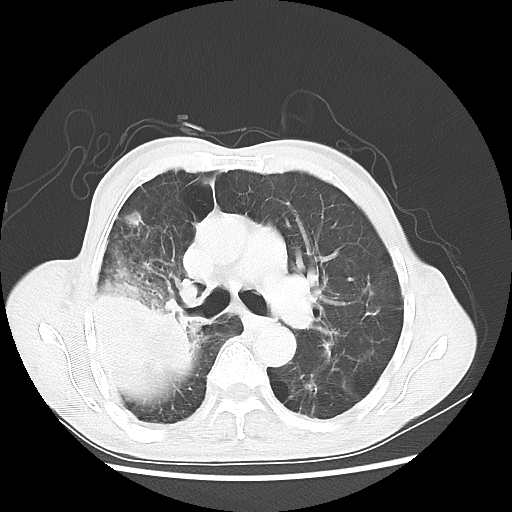
Chest CT, one axial slice; slice 33 of 58 in the series (ordered by position); 100 kVp; lung window (W 1500 / L -600 HU); 512 × 512 image matrix, field of view 351 × 351 mm. Male patient, age 75 years. From the clinical record (not read from this slice): clinical TNM (as recorded): T4 N1 M1.
Annotated regions visible in this slice (rectangle marked by the reading radiologist):
- lung tumour (recorded histology: adenocarcinoma): bounding box <85,267,203,405> (left, top, right, bottom; pixels)